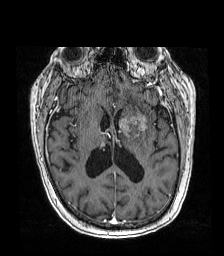
Brain MRI from a brain-tumour surgery series, one axial slice; slice 80 of 192 in the series (ordered by position); T1-weighted post-contrast; 1 mm slice thickness; 224 × 256 image matrix, field of view 219 × 250 mm. Case-level facts recorded for this patient, not image findings: histopathology: Metastatic carcinoma from lung primary.
Structures marked on this image (expert manual segmentation):
- tumour: bounding box [x1, y1, x2, y2] px = [117, 112, 148, 137]